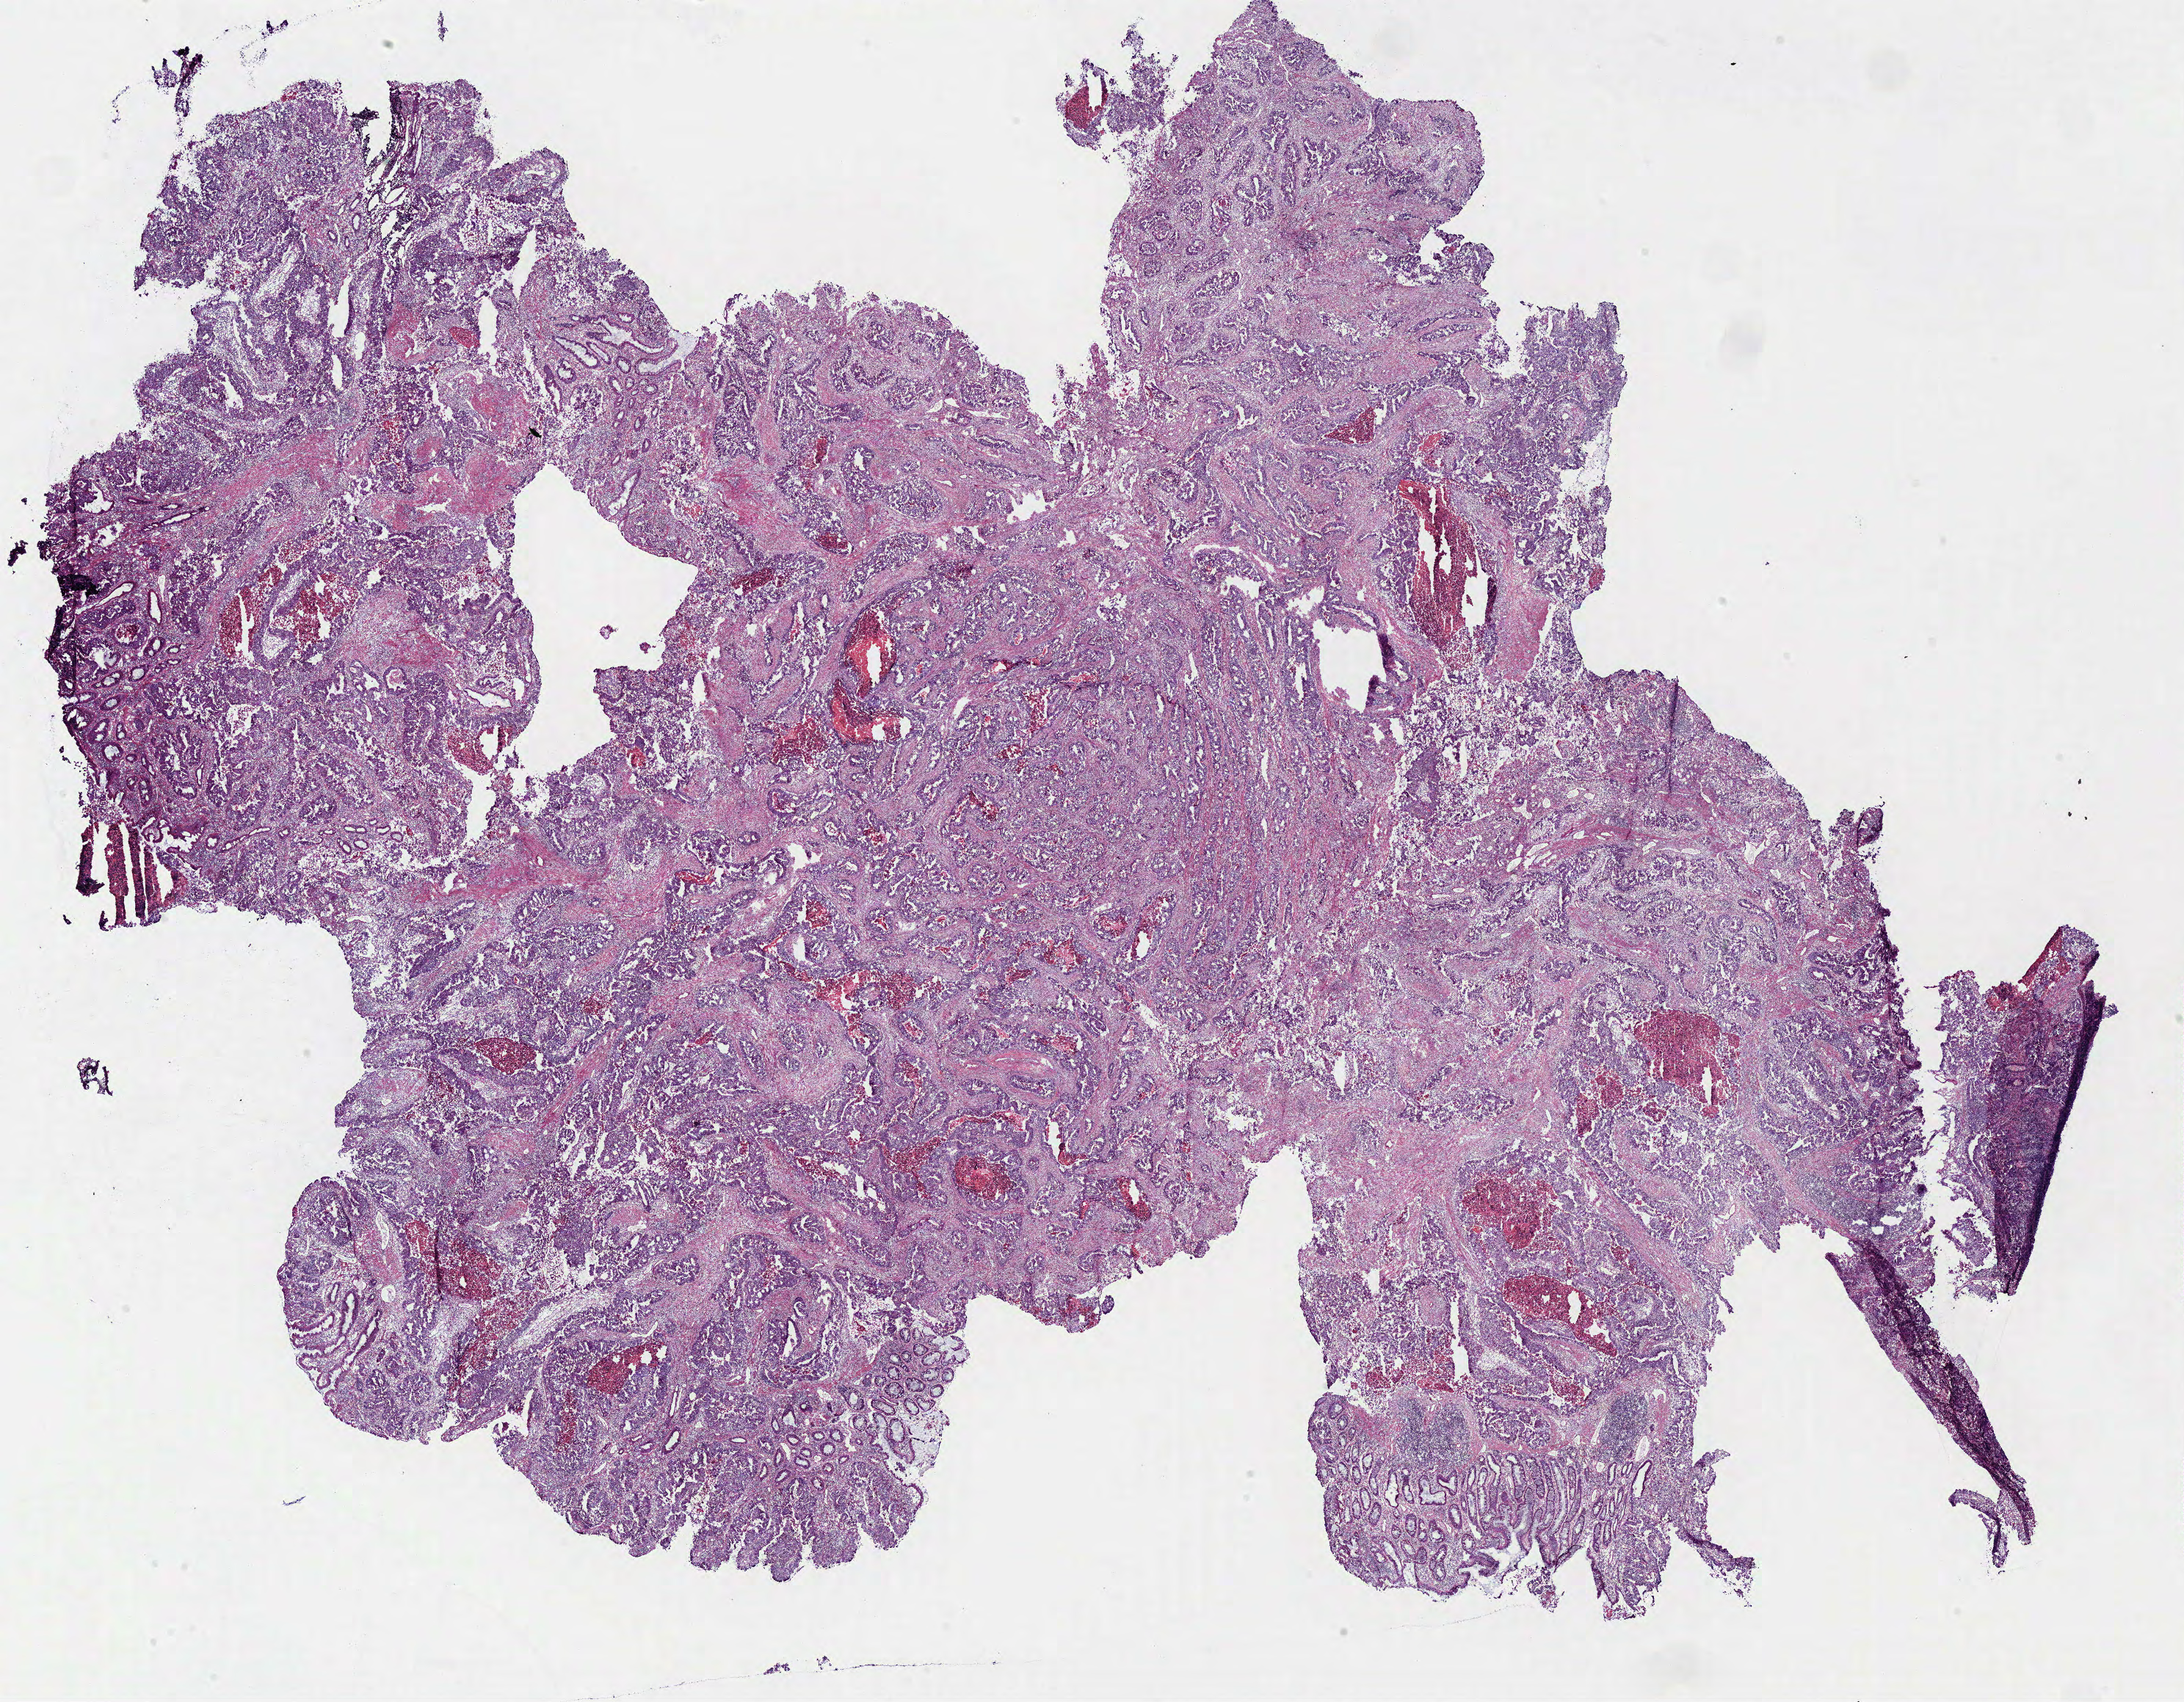
Whole-slide histology image, Hematoxylin and eosin (H&E) stained — low-resolution overview of the scanned area, about 23.4 x 18.3 mm (acquisition: 40x scan). Frozen section from the bottom of the tissue portion. Rectum, primary tumour sample. Female, age 62 years at initial diagnosis. Slide review estimates, as recorded: tumour cells 85%, tumour nuclei 75%, normal cells 10%, stromal cells 0%, necrosis 5%. Infiltration values recorded for this section: lymphocyte infiltration 10%, monocyte infiltration 1%, neutrophil infiltration 2%.
Histologic diagnosis: Adenocarcinoma, NOS. AJCC pathologic stage: IIIB (7th edition). Lymph nodes positive (case pathology): 1 of 19 examined.